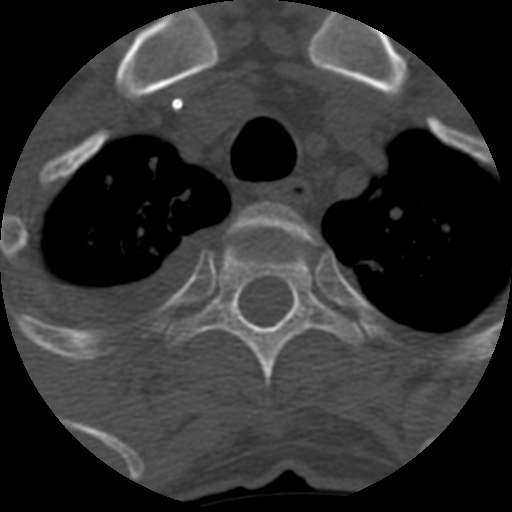
CT including the spine, one axial slice. Slice 491 of 708 in the series (ordered by position). Reconstruction kernel STANDARD. 120 kVp. One of 3 acquisitions stored at this slice position. Bone window (W 1800 / L 400 HU). 1.25 mm slice thickness. 512 × 512 image matrix, field of view 160 × 160 mm. Patient age 55 years. Case-level facts recorded for this patient, not image findings: primary cancer: colon; vertebrae with lytic lesions (as recorded): T12, L1, L5.
Structures marked on this image (semi-automatic segmentation, software-assisted and operator-edited):
- T2 vertebra: box from (x=230, y=202) to (x=313, y=243) px
- T3 vertebra: (x=164, y=241)–(x=362, y=389)